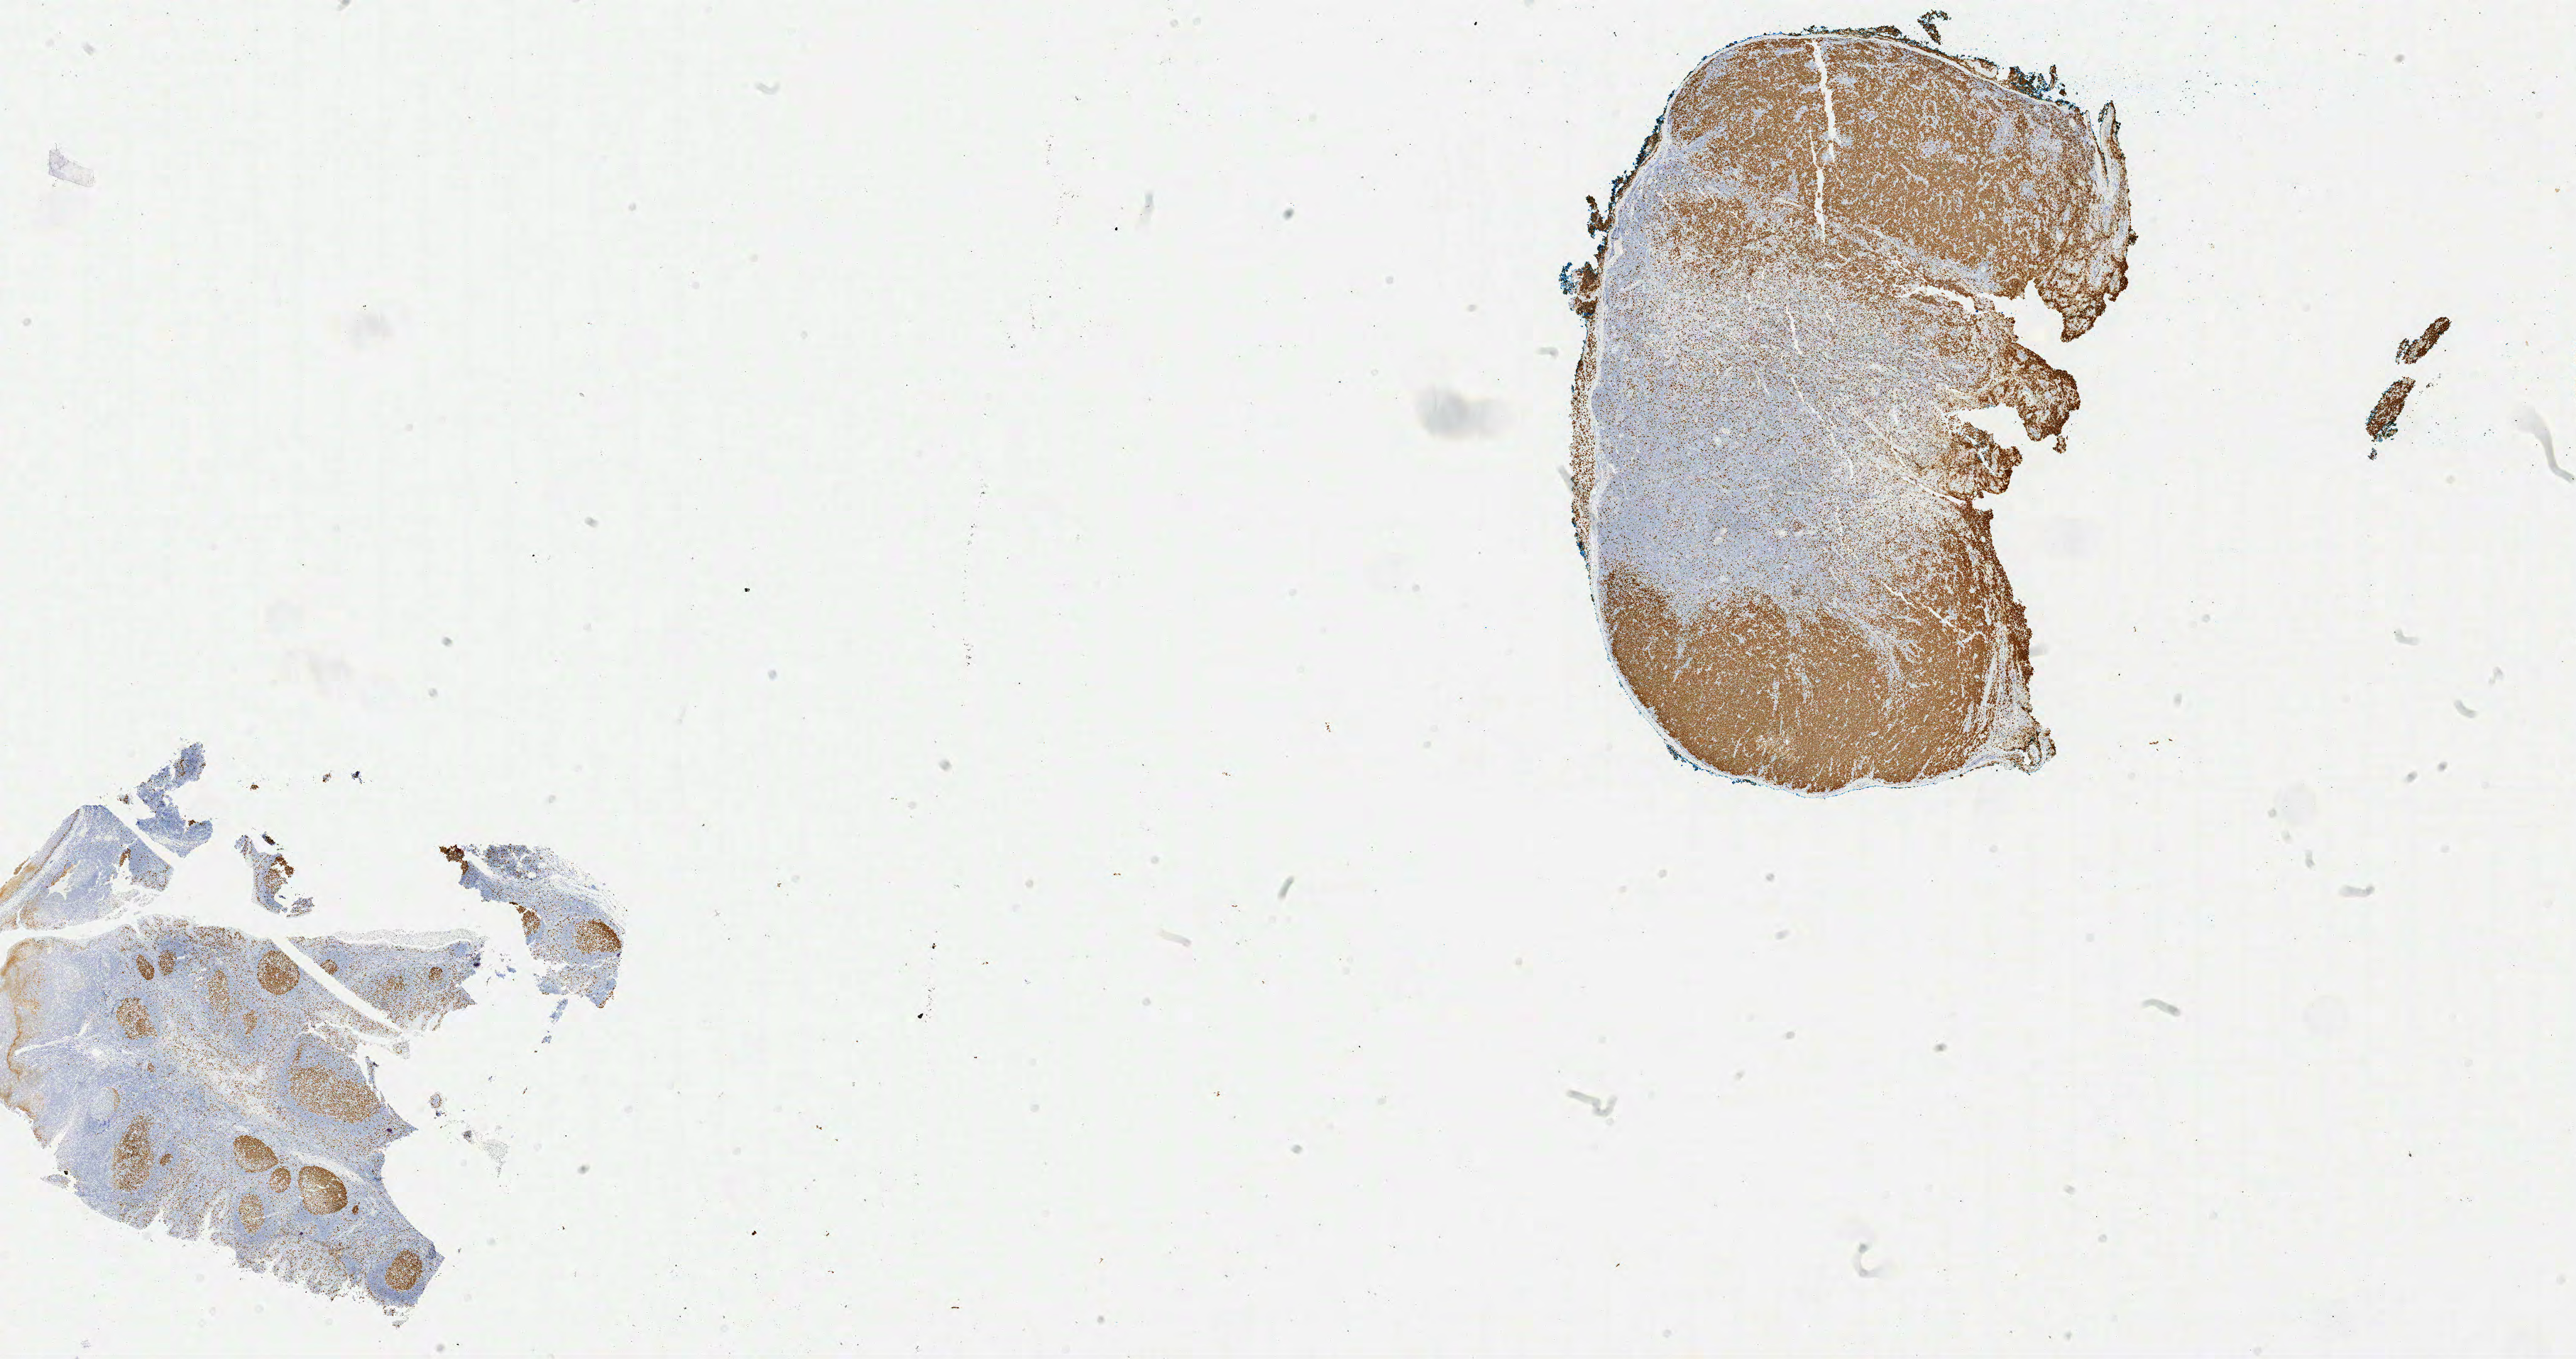
Immunohistochemistry (IHC) whole-slide image stained for Ki-67 — whole scanned area (about 28.9 x 15.3 mm) shown as a low-resolution overview. Specimen: tumor tissue. Patient: male, aged 47.
Diagnosis: Burkitt lymphoma, NOS.